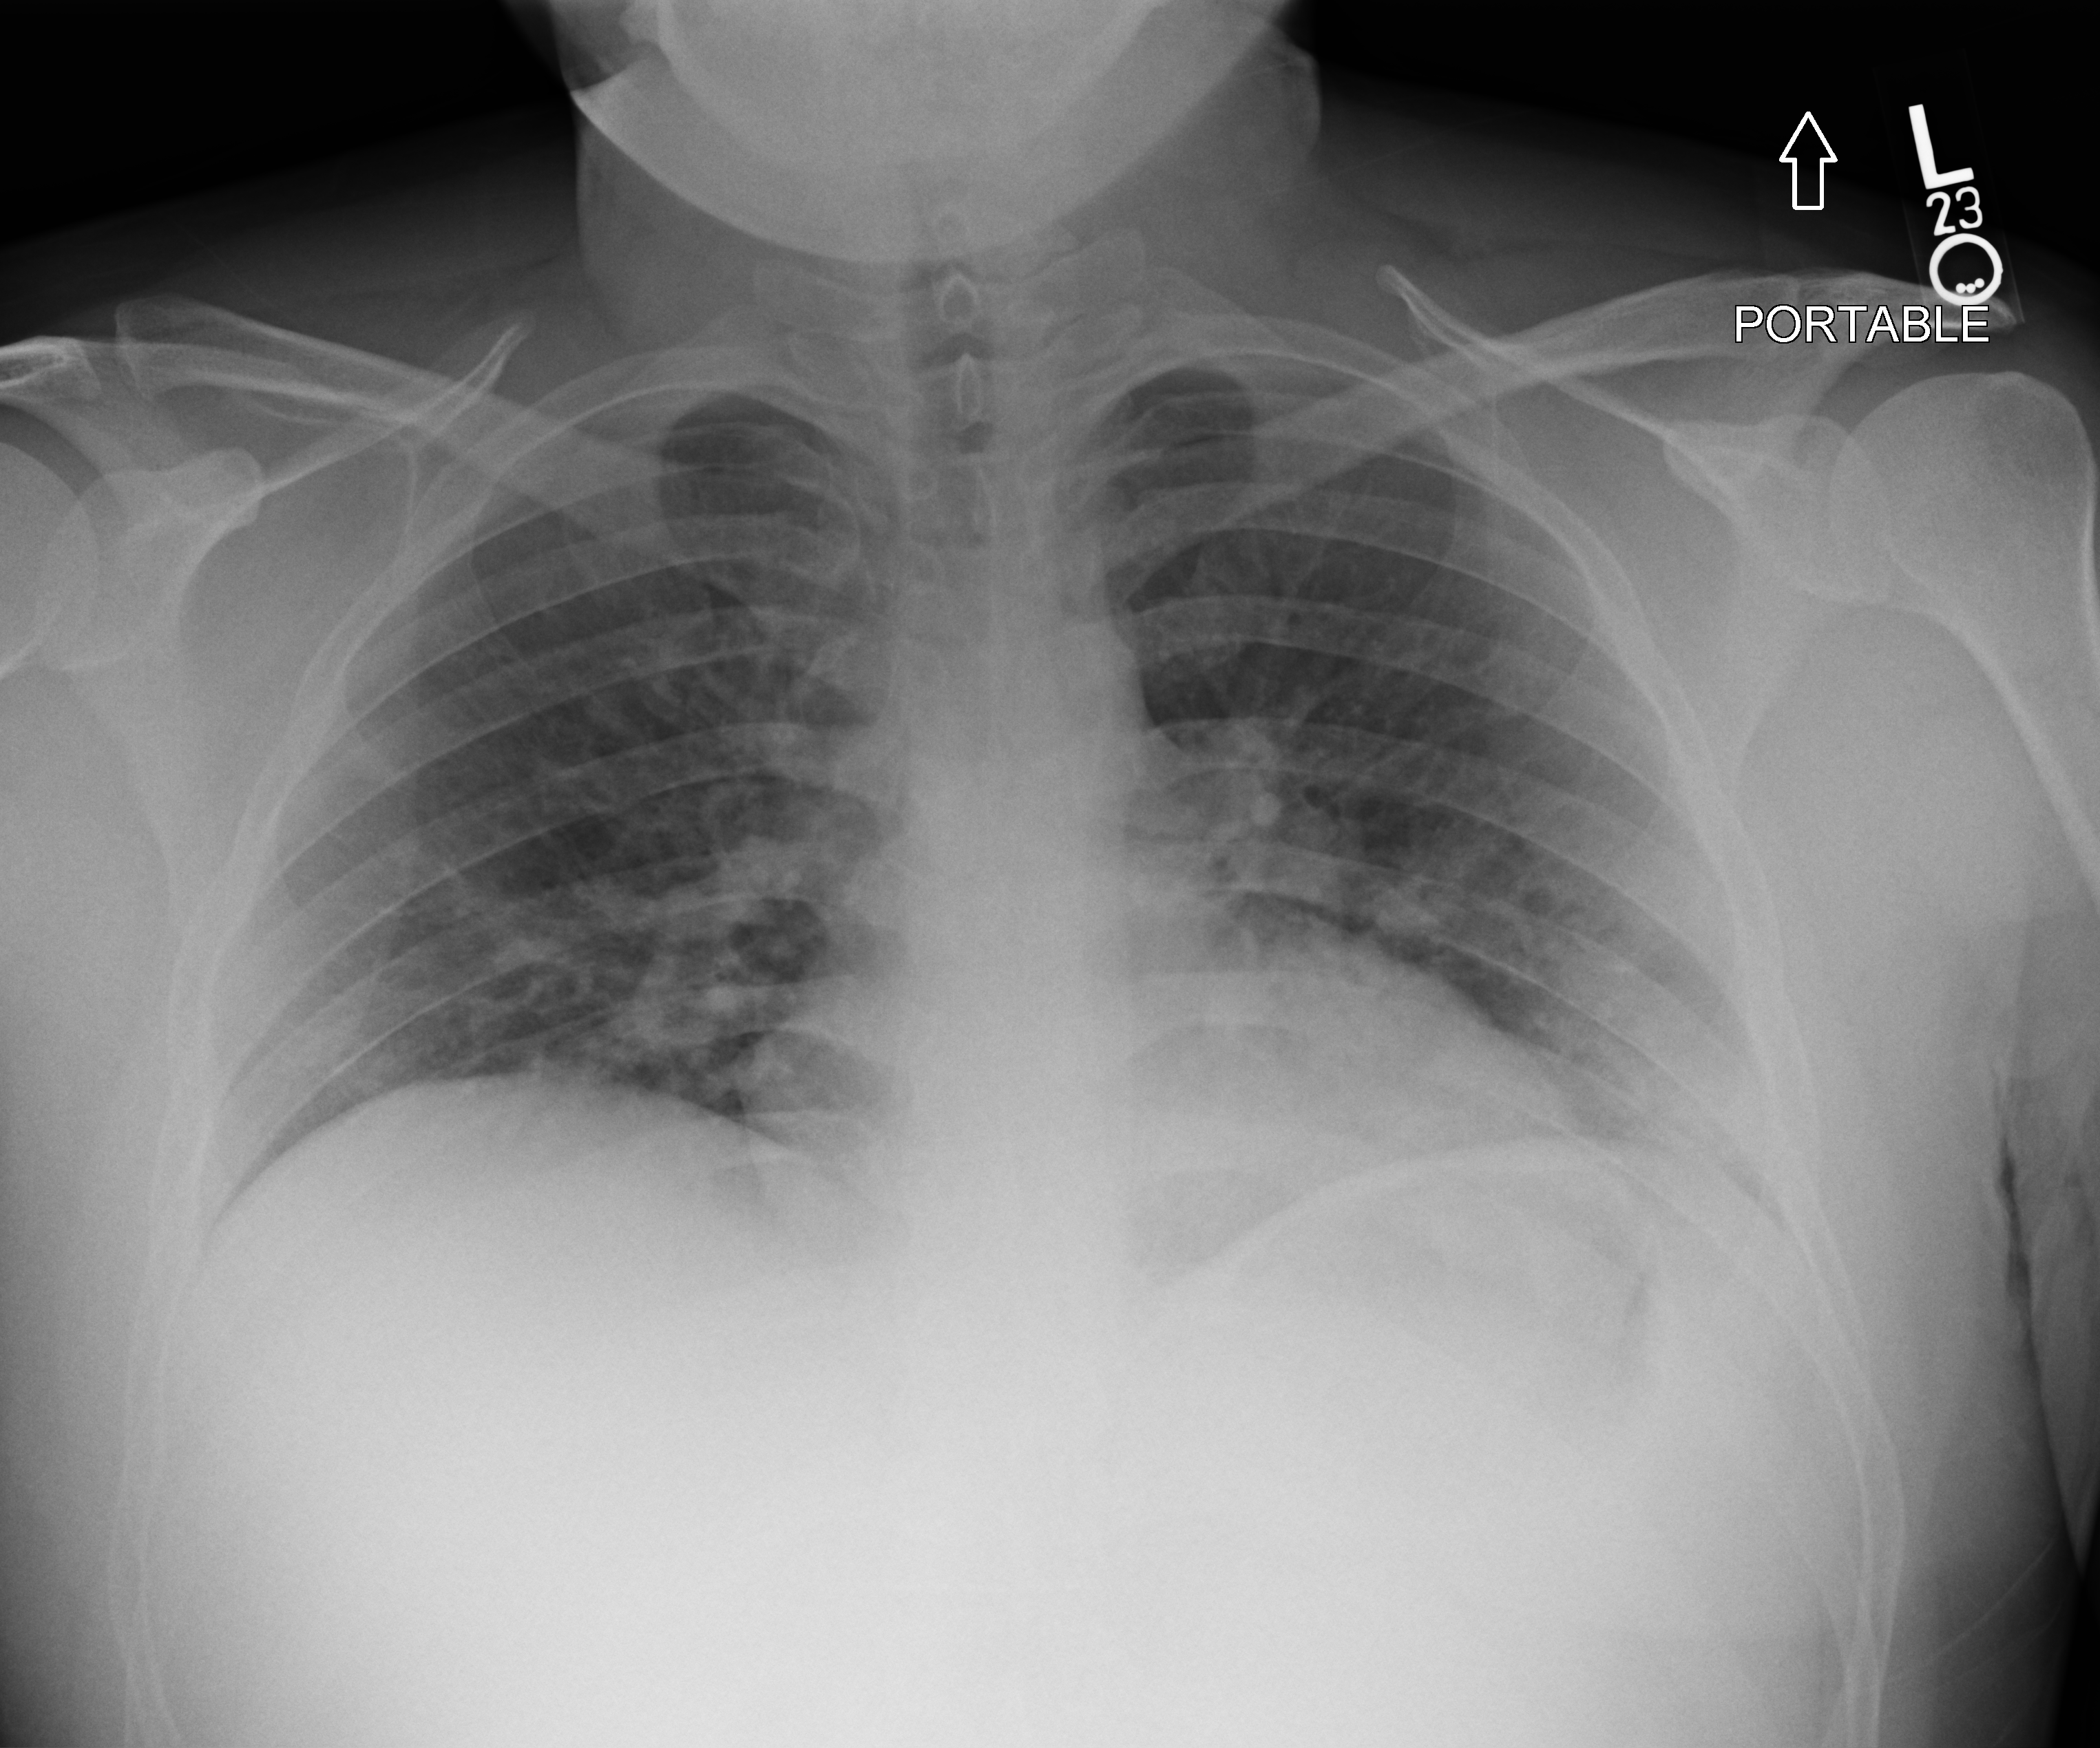
Chest X-ray (portable), anteroposterior (AP) projection. Patient hospitalised with COVID-19; male, aged 18–59 years.
Hospital-stay facts (about this admission, not read from this image; timing relative to this image not recorded): mechanically ventilated during this hospital stay: no; admitted to intensive care during this hospital stay: no.